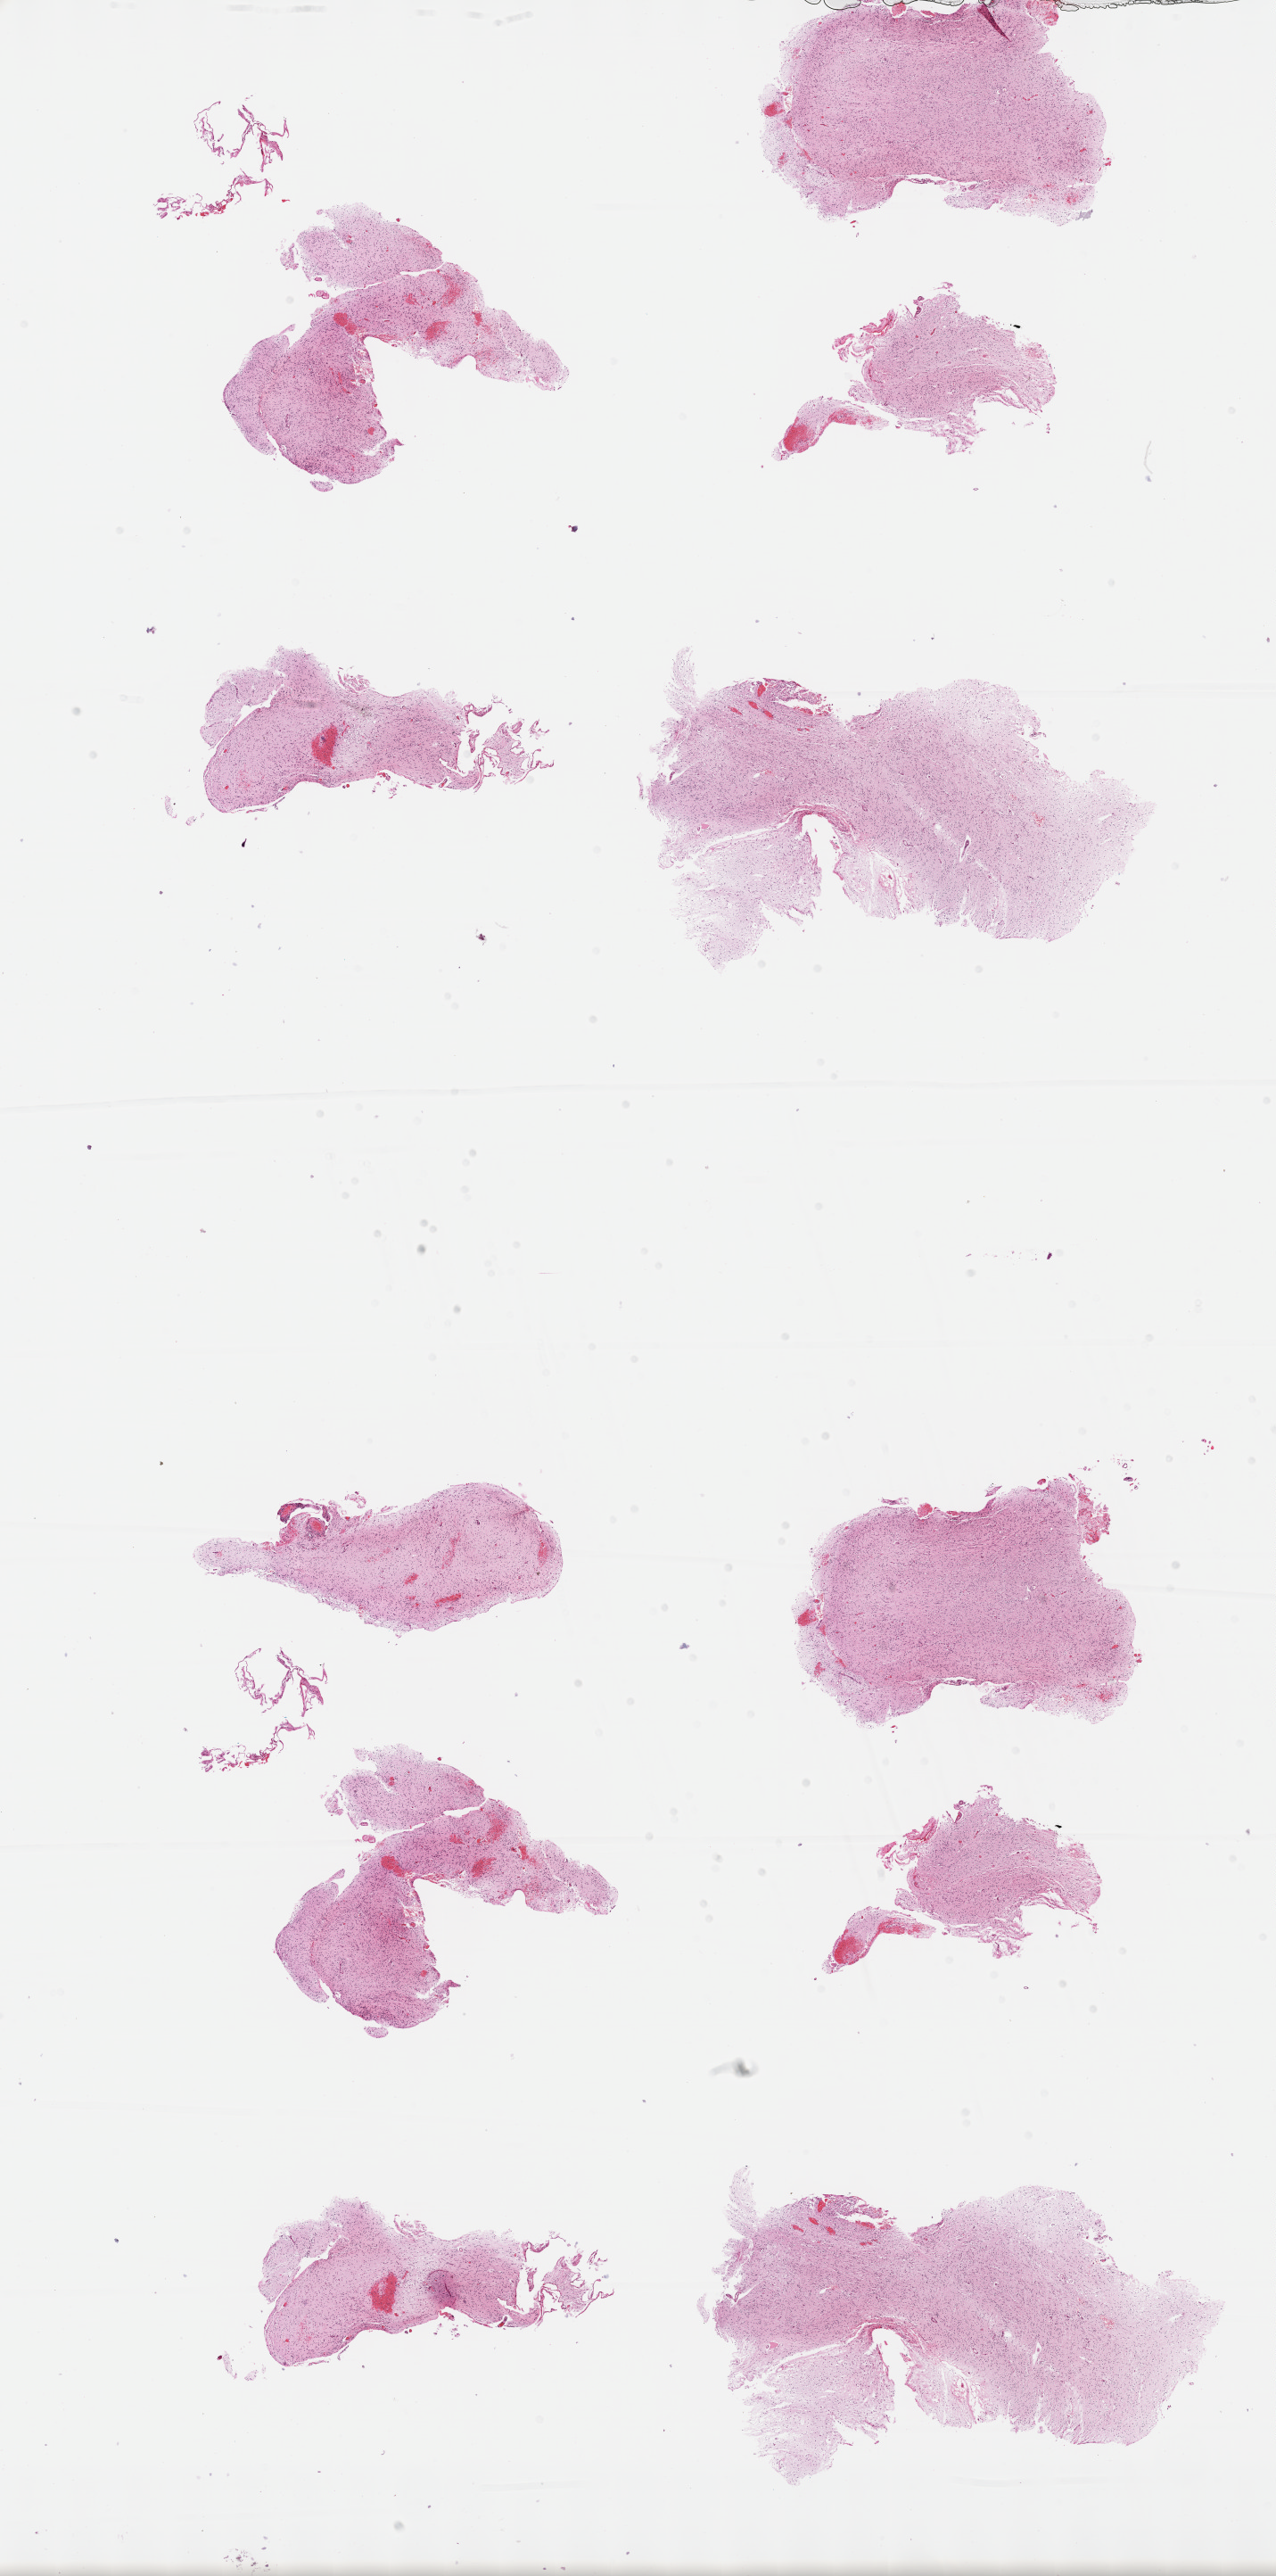
Whole-slide histology image, Hematoxylin and eosin (H&E) stained — whole scanned area (about 11.6 x 23.4 mm, acquisition: 40x scan) shown as a low-resolution overview. Formalin-fixed paraffin-embedded (FFPE) diagnostic section. Primary tumour sample from the brain. Male, age 32 years at initial diagnosis. Histologic grade: G2 (moderately differentiated).
Diagnosis: Astrocytoma, NOS (cerebrum).